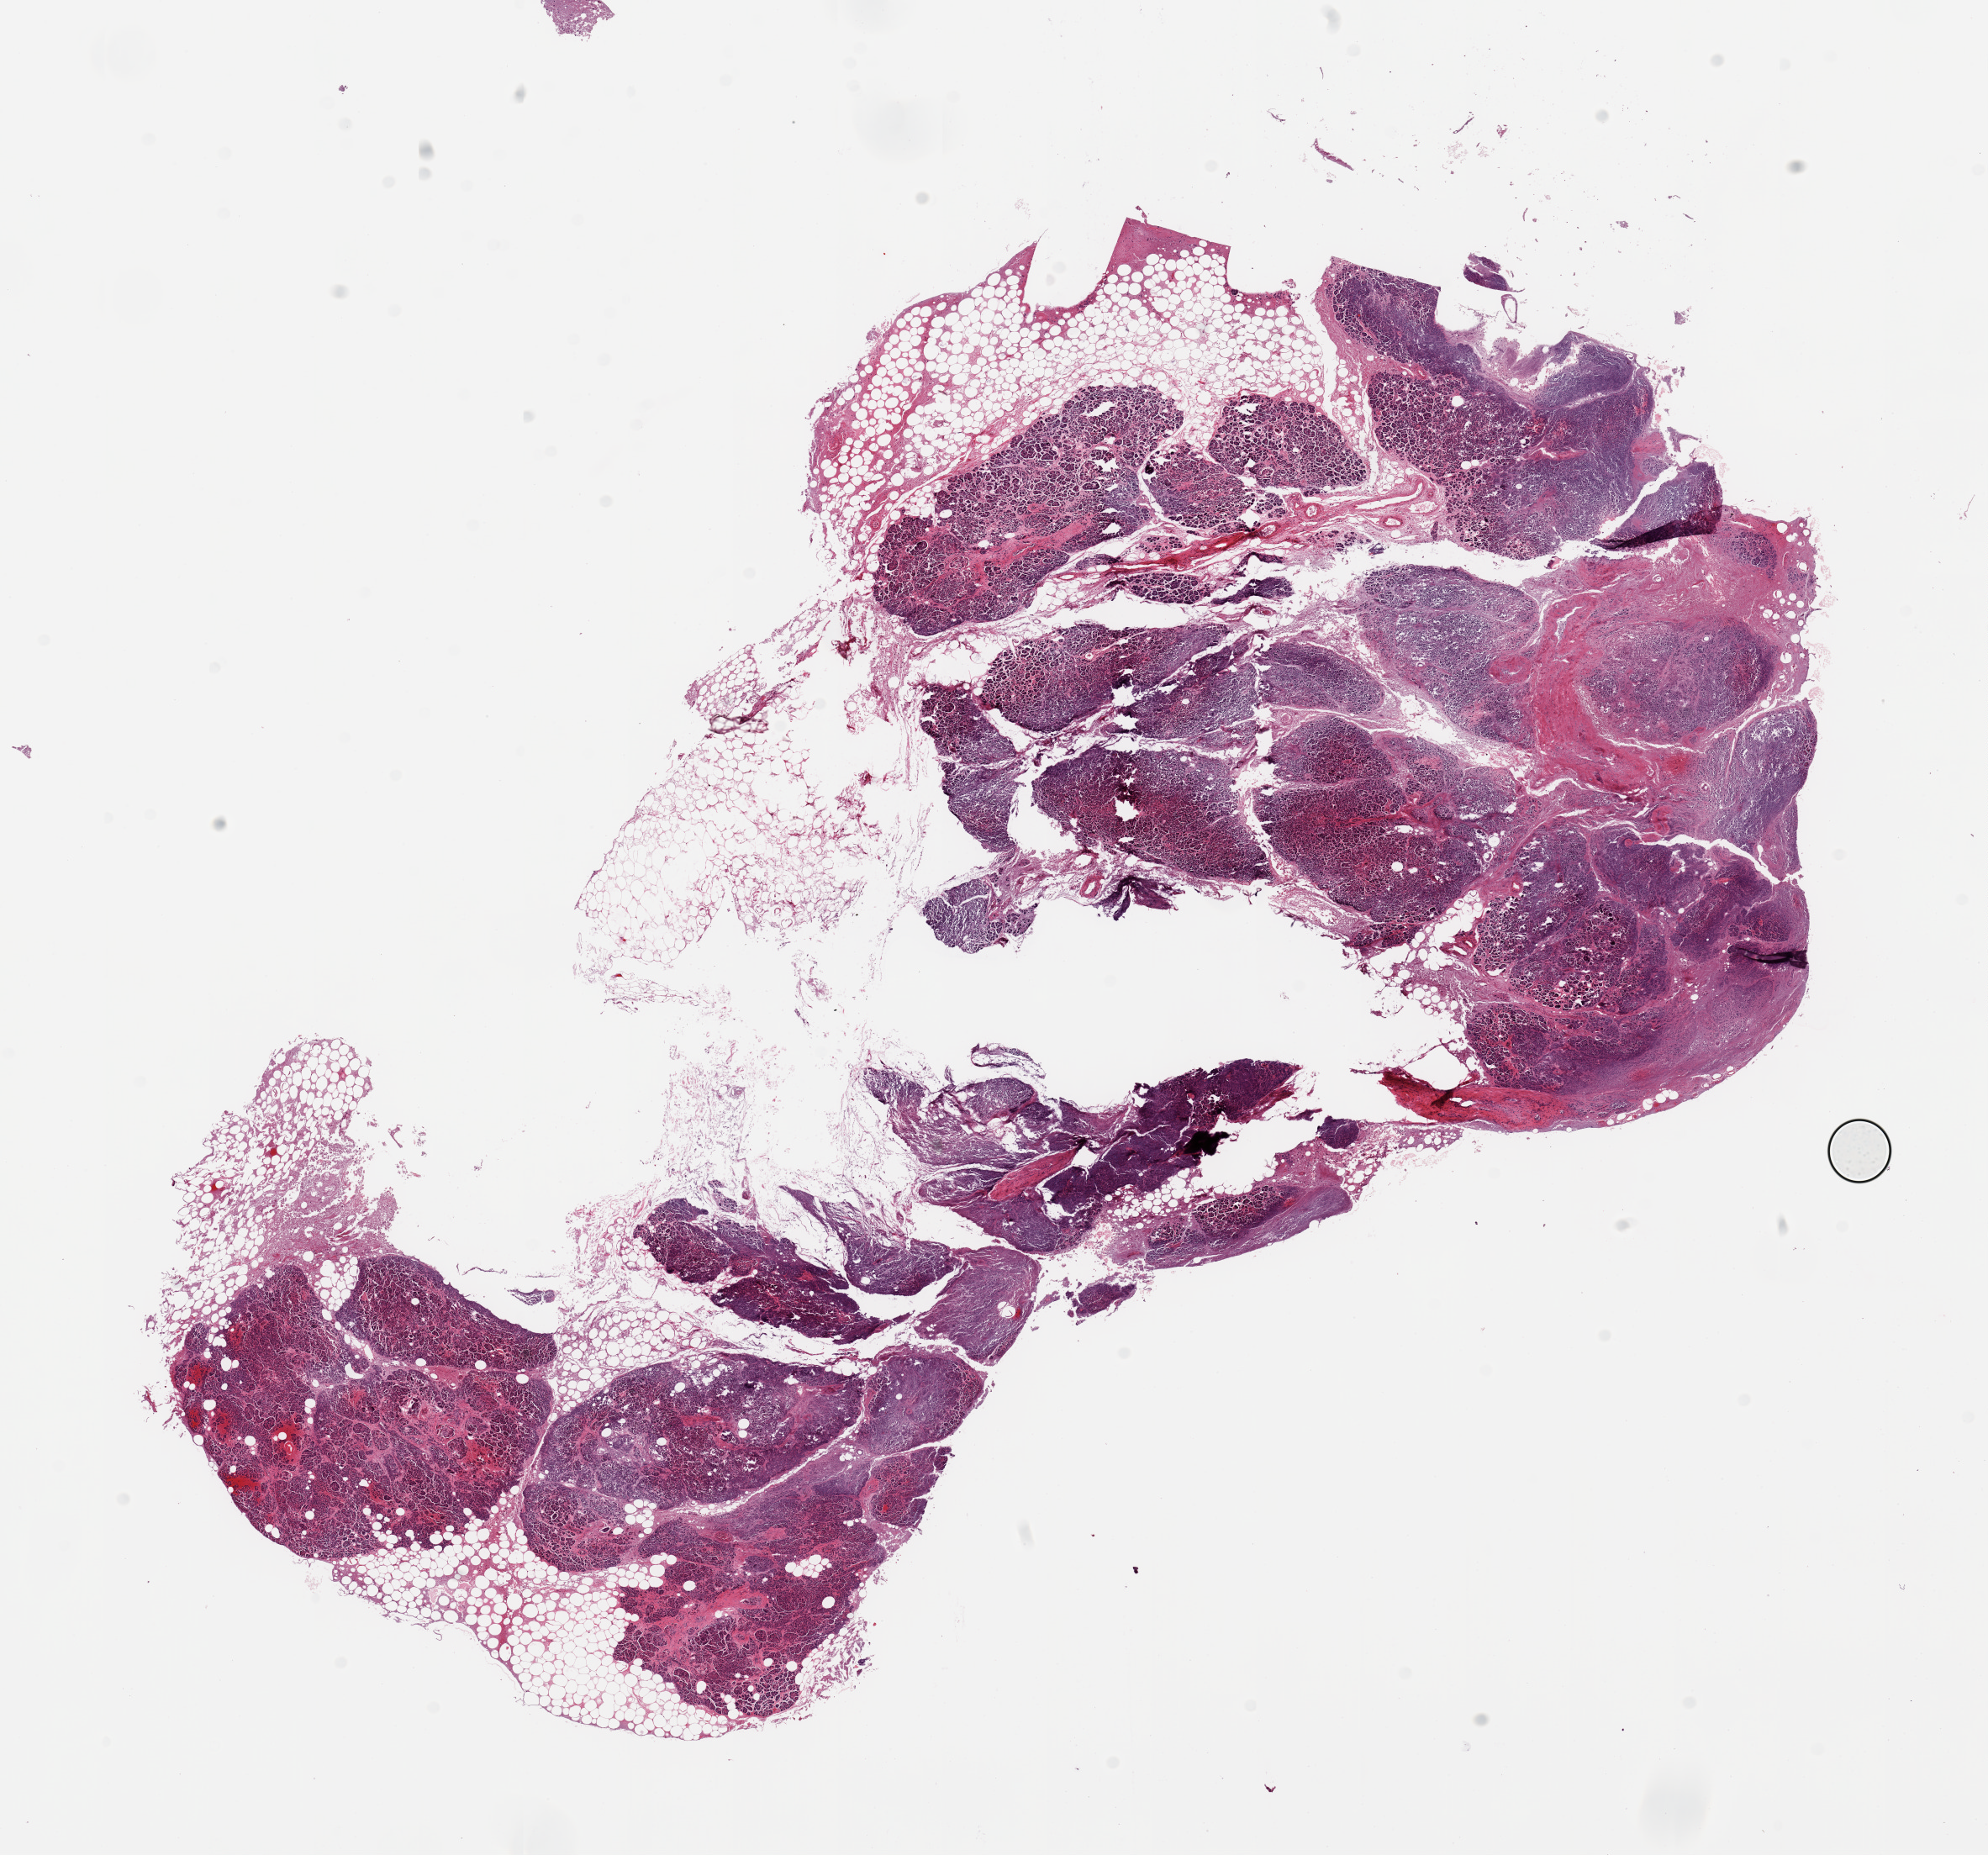
H&E whole-slide image, low-resolution overview of the scanned area, about 18.7 x 17.5 mm, PAXgene-fixed, paraffin-embedded tissue, sampled site (target tissue): pancreas, donor tissue sample. Male donor.
Reviewer comment on this tissue sample: 1 piece, severely autolyzed/saponified.